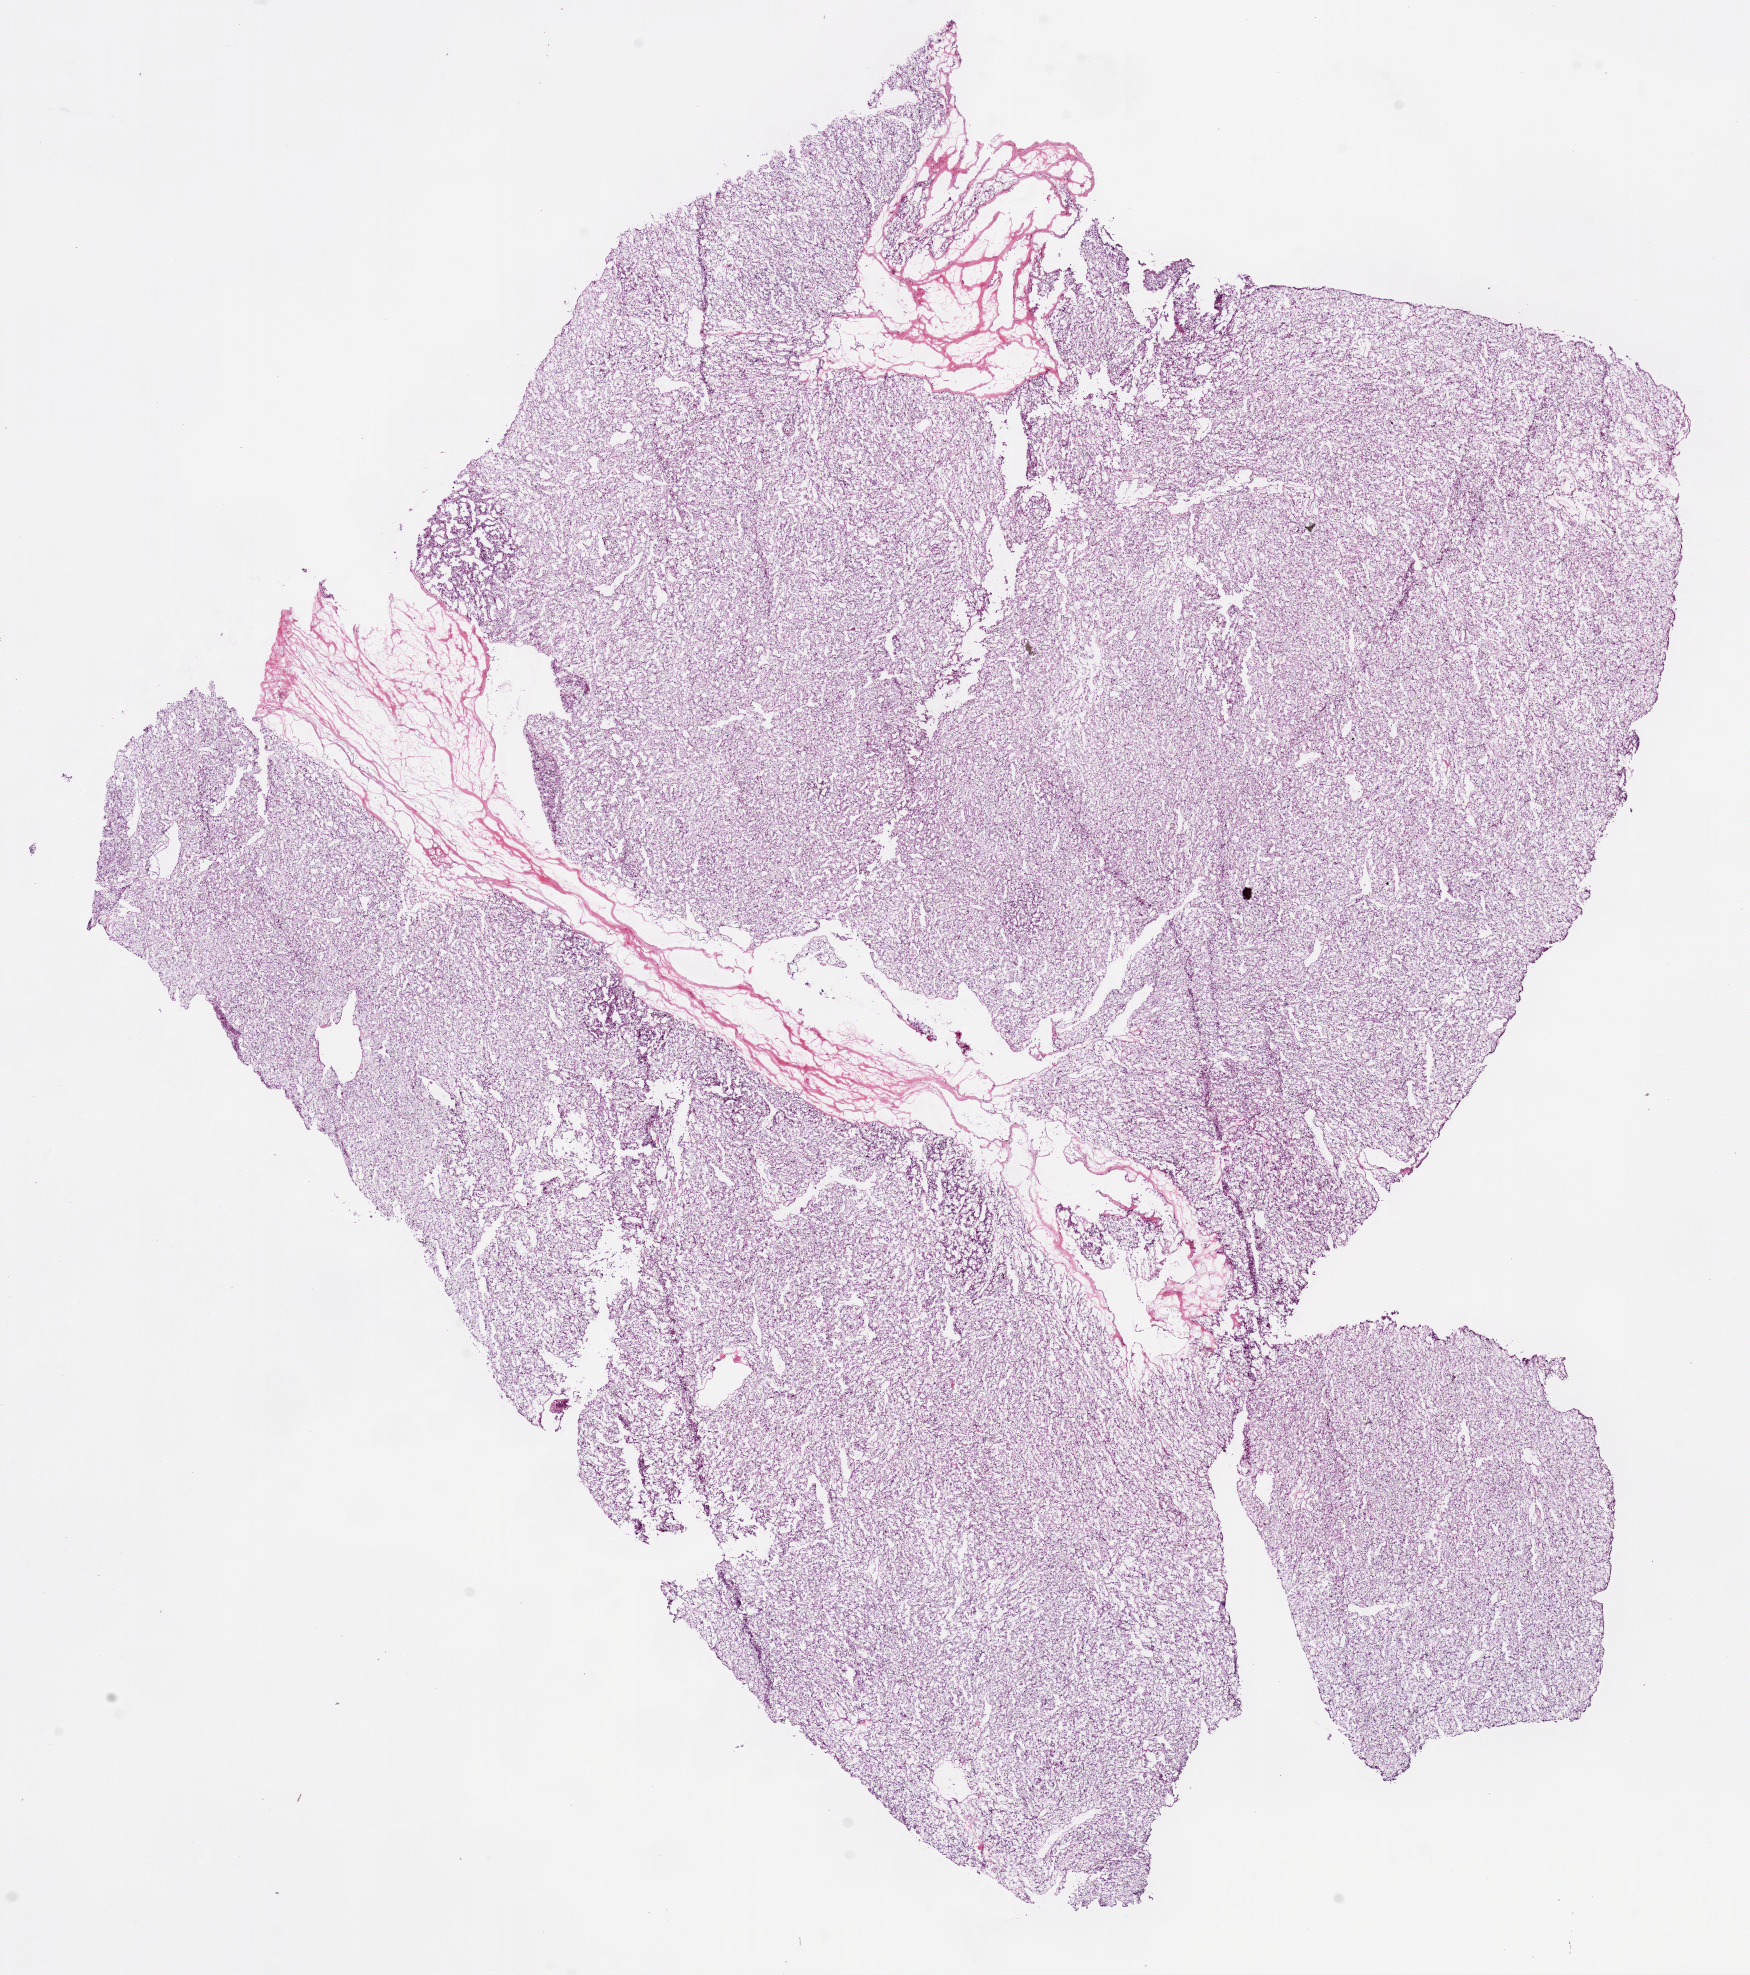
Digitized H&E tissue section (whole slide) — whole scanned area (about 14.0 x 15.8 mm, slide scanned at 20x) shown as a low-resolution overview, frozen section from the bottom of the tissue portion, kidney, primary tumour sample. Male, age 74 years at initial diagnosis. Histologic grade: G3 (poorly differentiated). Pathologist review of this section (percent, as recorded): tumour cells 92%, tumour nuclei 85%, normal cells 0%, stromal cells 8%, necrosis 0%. Inflammatory infiltration, as recorded: lymphocyte infiltration 2%, monocyte infiltration 0%, neutrophil infiltration 0%.
- TNM: T2 N0 M0
- laterality: left
- lymph nodes positive (case pathology): 0 of 13 examined
- diagnosis: Clear cell adenocarcinoma, NOS
- AJCC pathologic stage: II (6th edition)